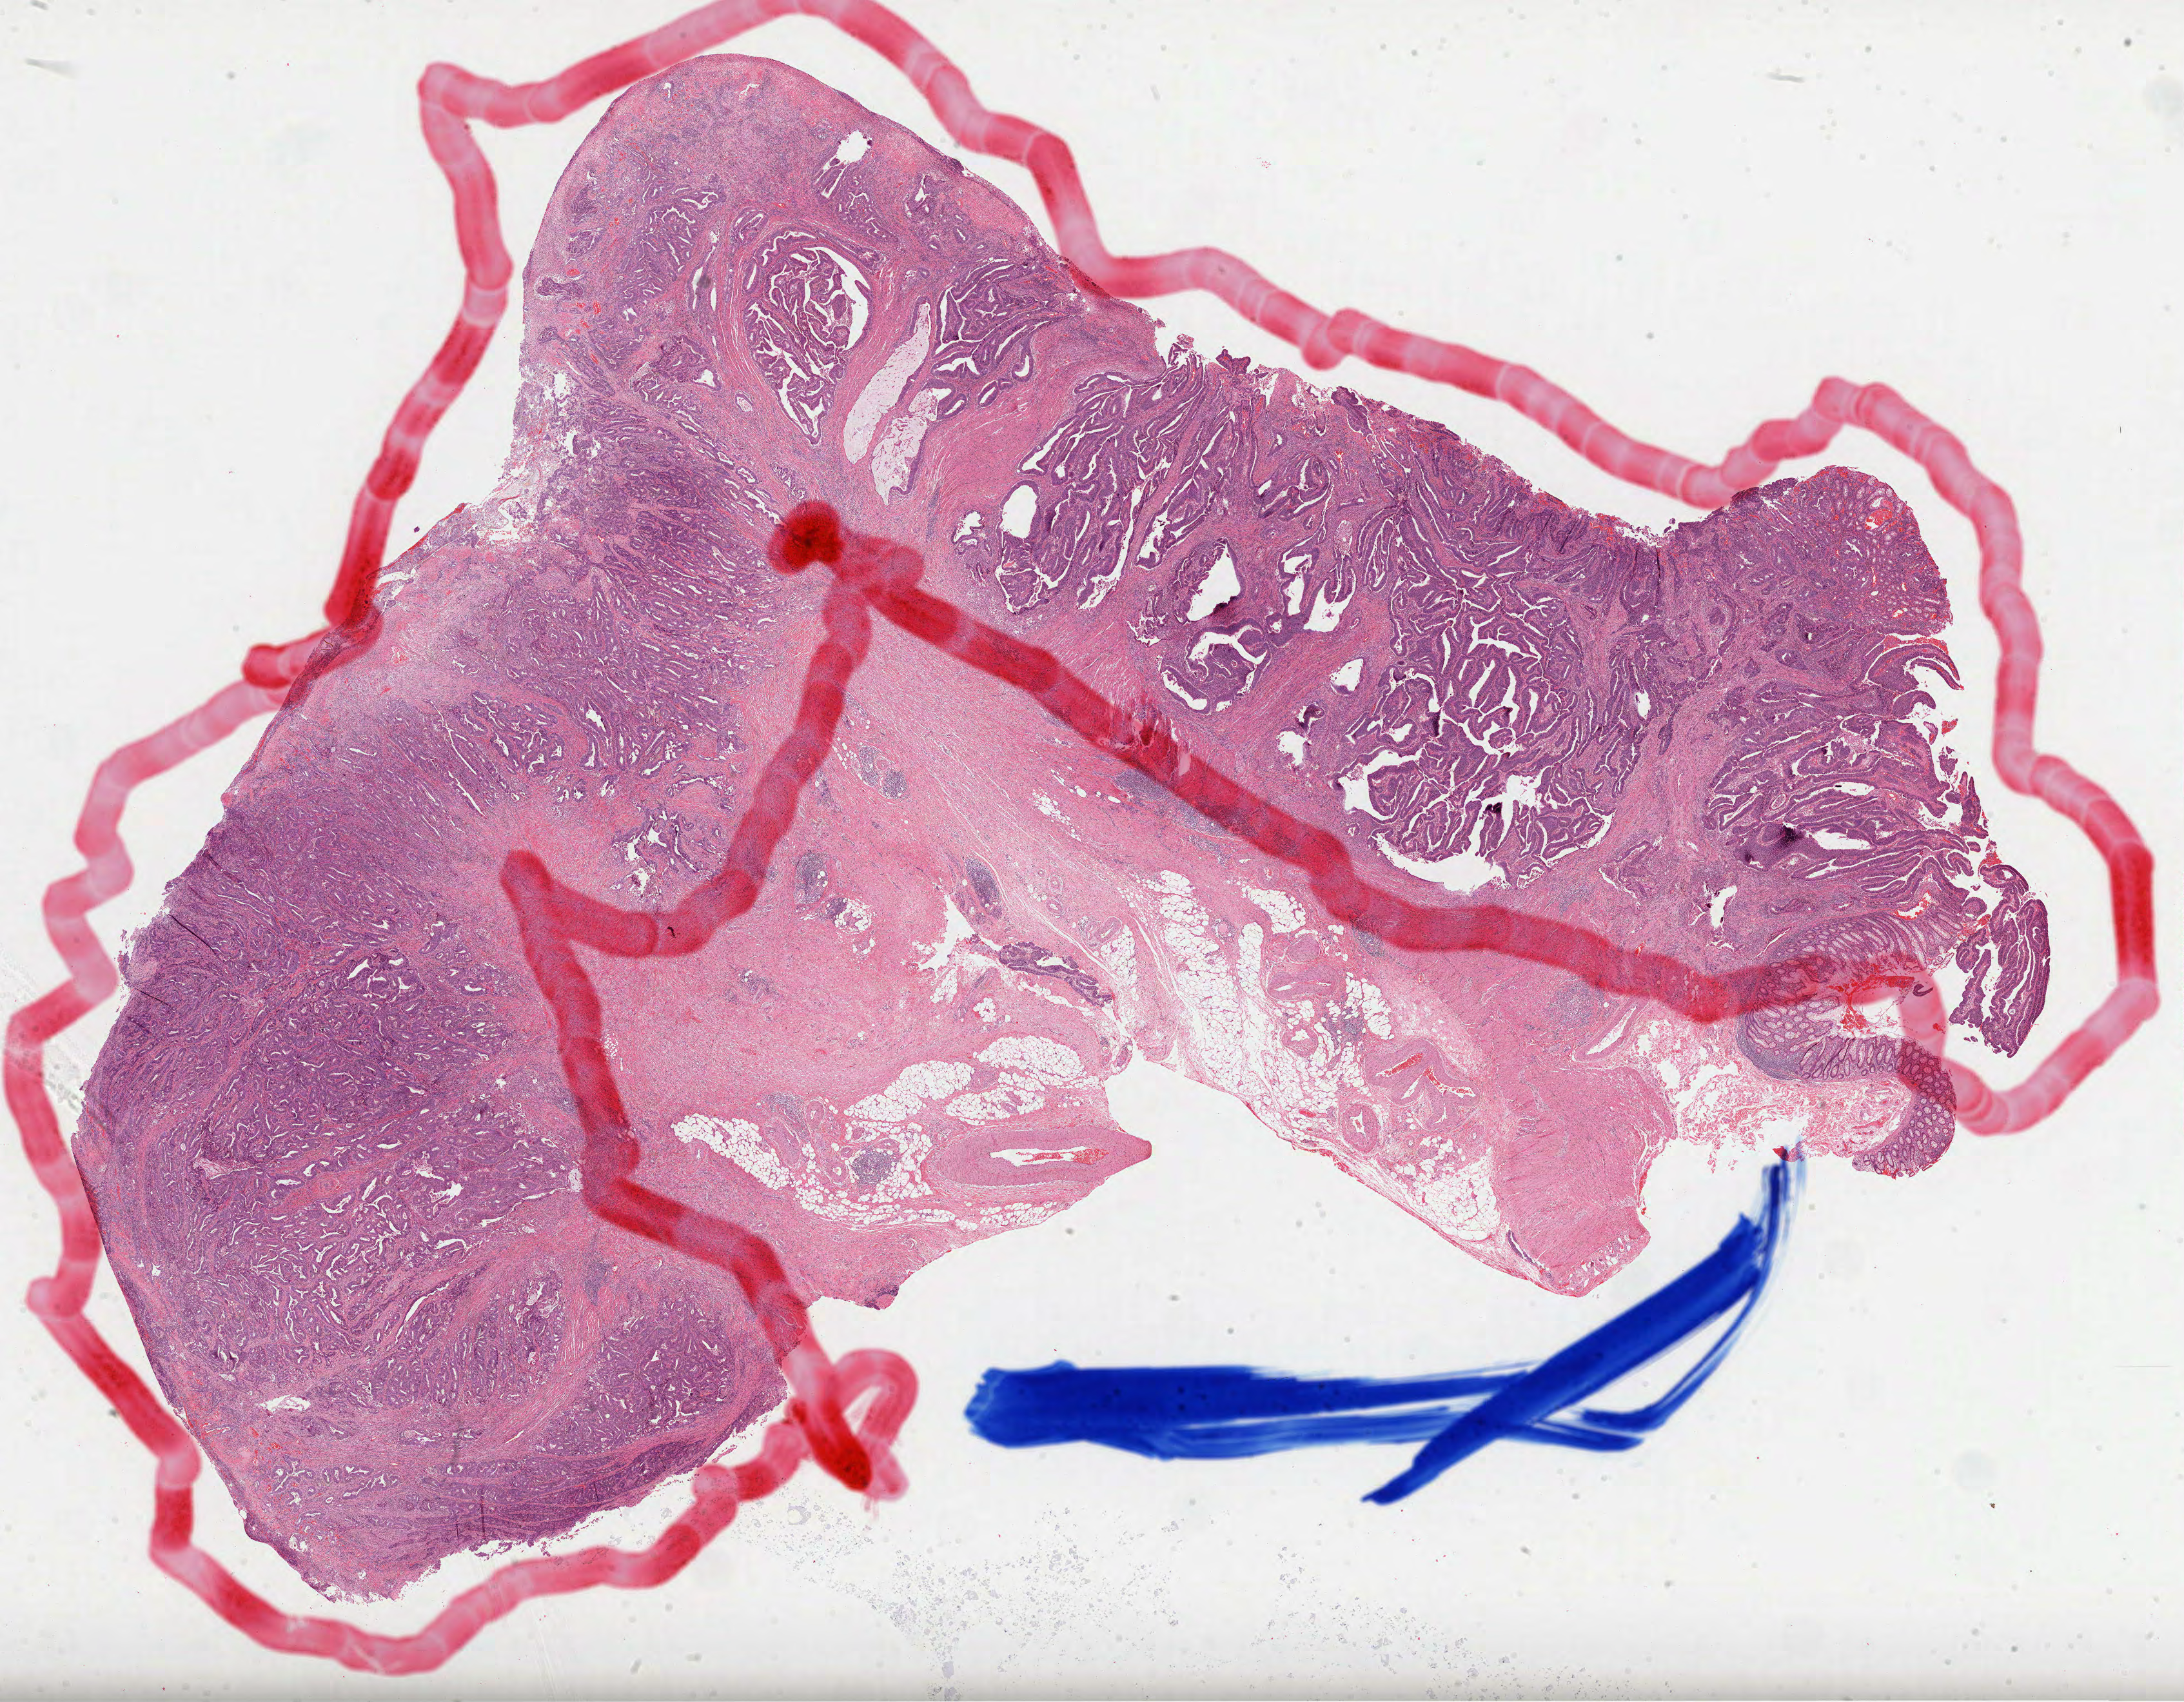
Whole-slide histology image, H&E, a low-resolution overview of the entire scanned area, about 27.3 x 21.3 mm; formalin-fixed paraffin-embedded (FFPE) diagnostic section; sample: primary tumour, colon. Patient: female, age at initial diagnosis 51 years.
* AJCC pathologic stage: IIIC
* diagnosis: Adenocarcinoma, NOS
* lymph nodes positive (case pathology): 12 of 12 examined